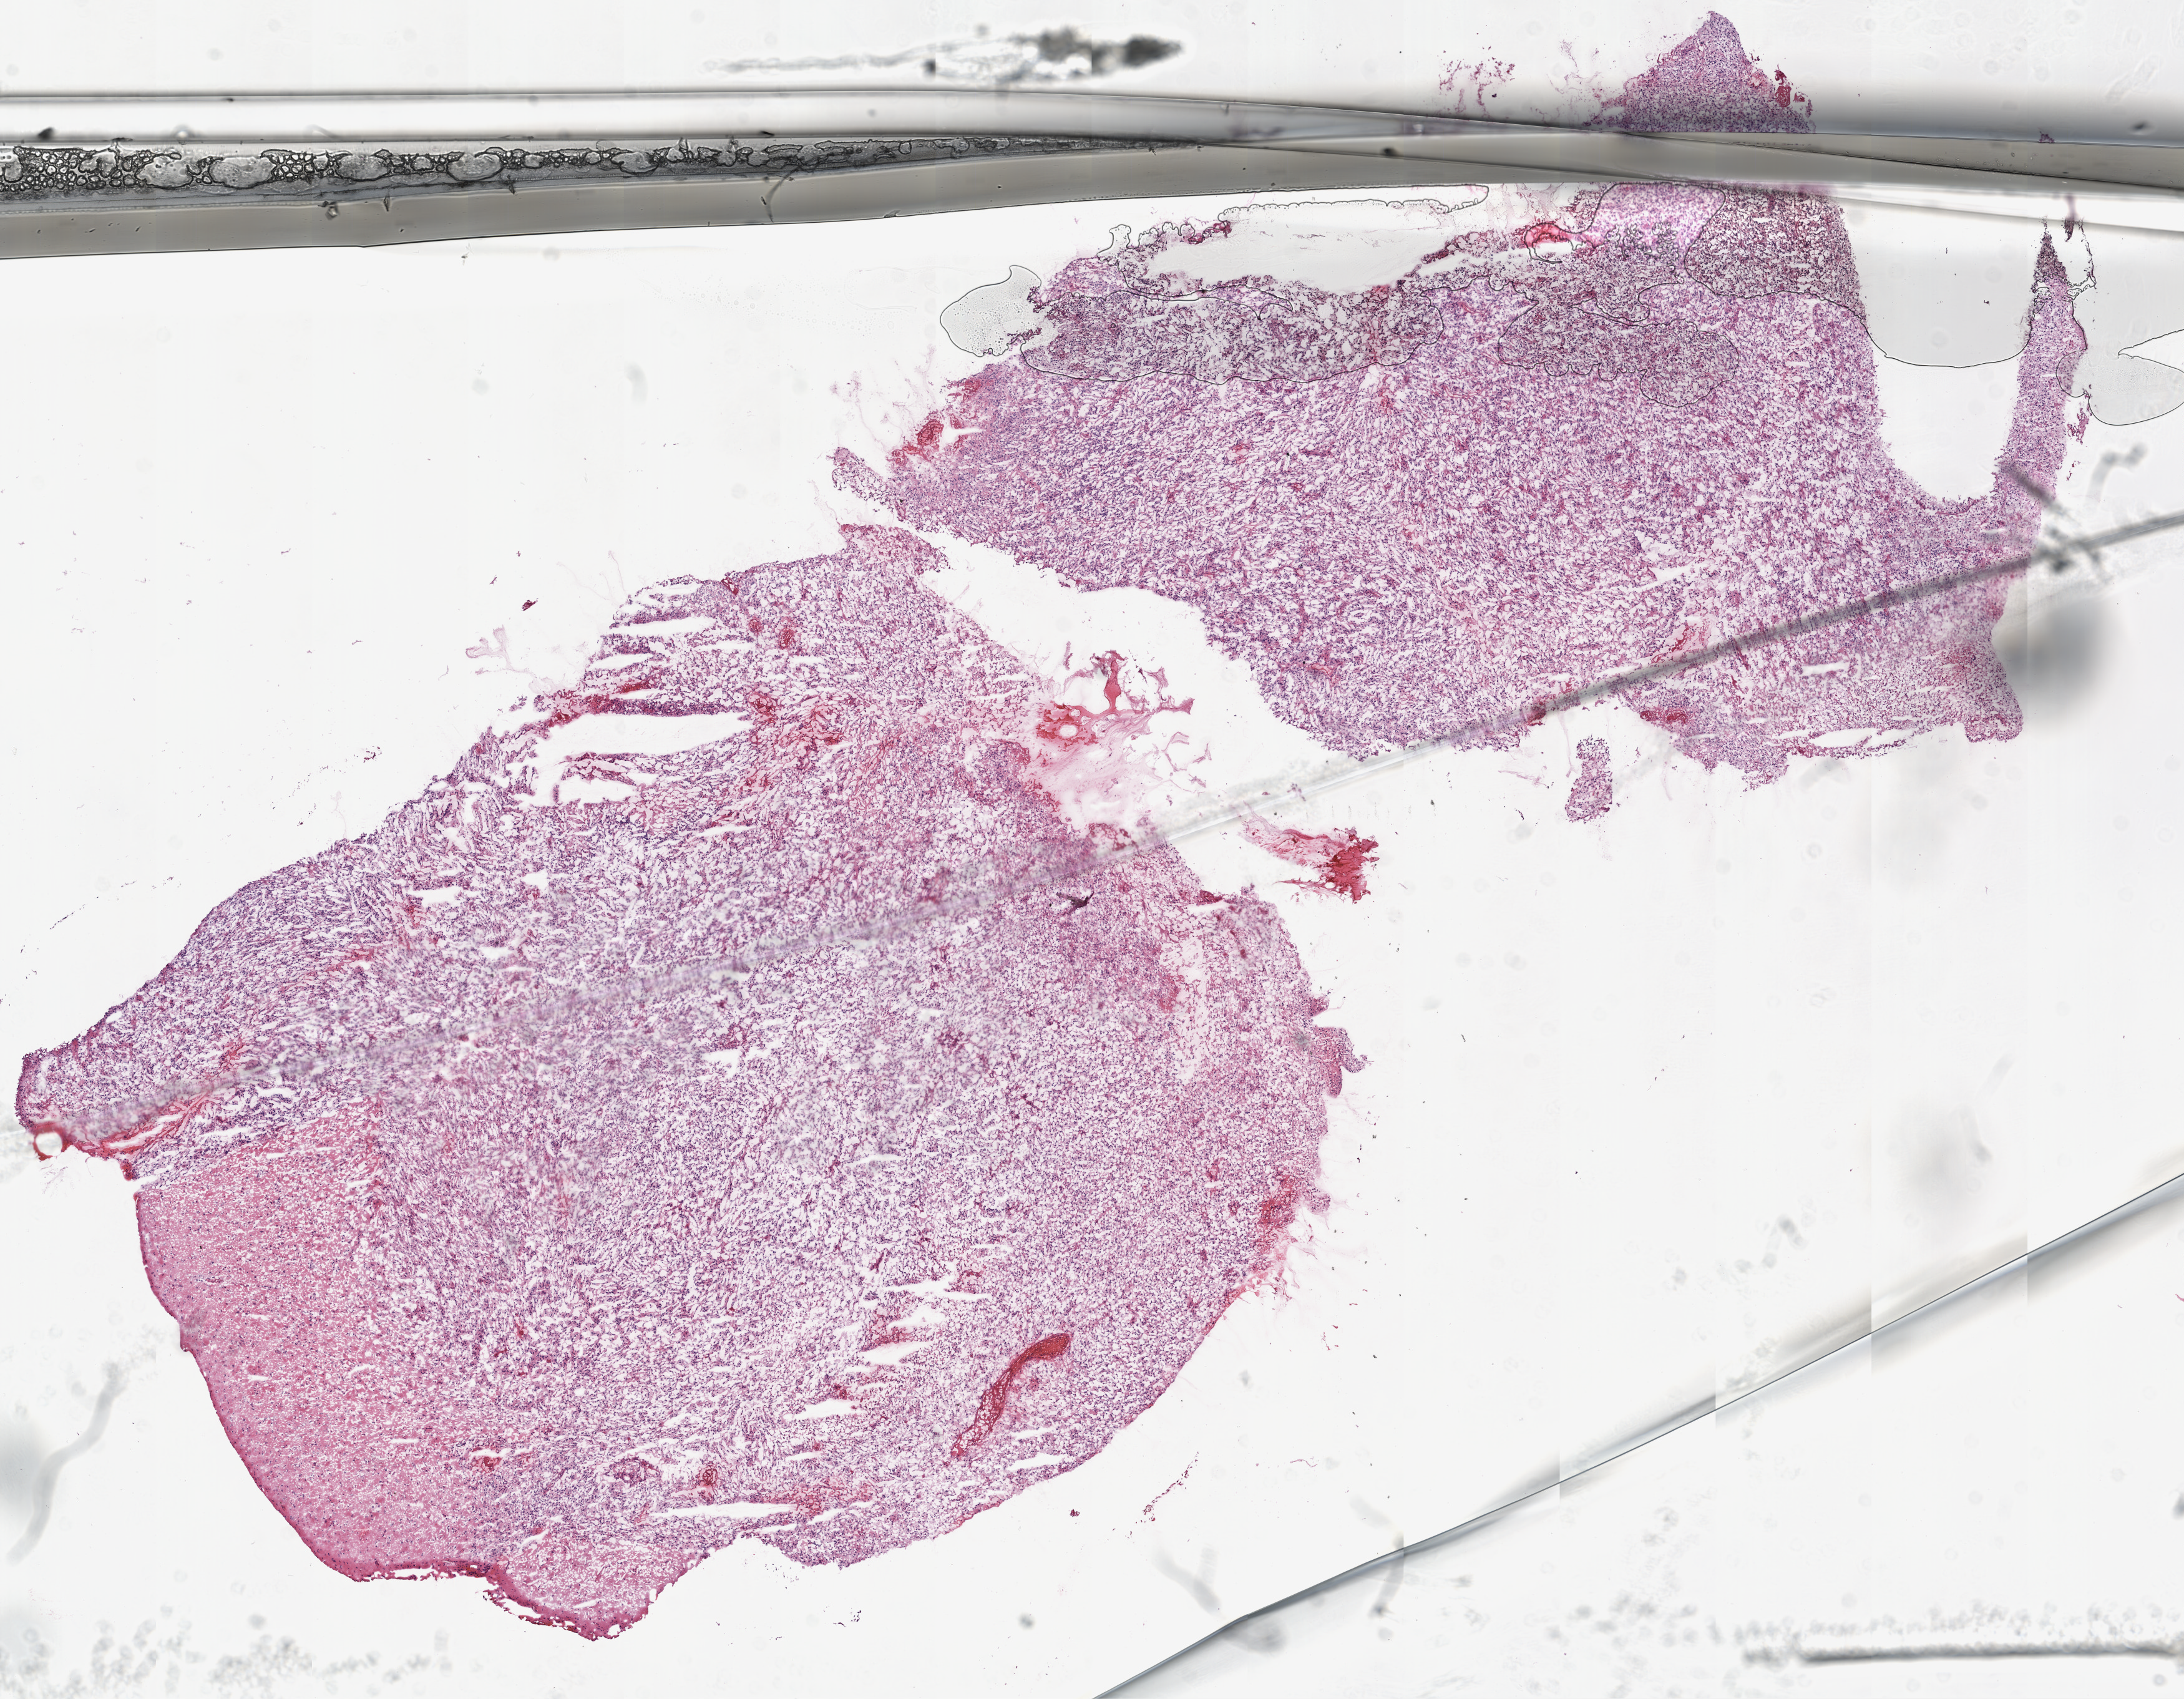
Digitized Hematoxylin and eosin (H&E) stained tissue section (whole slide) — shown as a low-resolution overview of the whole scanned area (about 14.0 x 10.9 mm, slide scanned at 20x). Frozen section. Primary tumour sample from the brain. Patient: female, age at initial diagnosis 52 years. Slide review estimates, as recorded: tumour cells 98%, tumour nuclei 85%, normal cells 0%, stromal cells 0%, necrosis 2%.
Pathologic diagnosis: Glioblastoma.